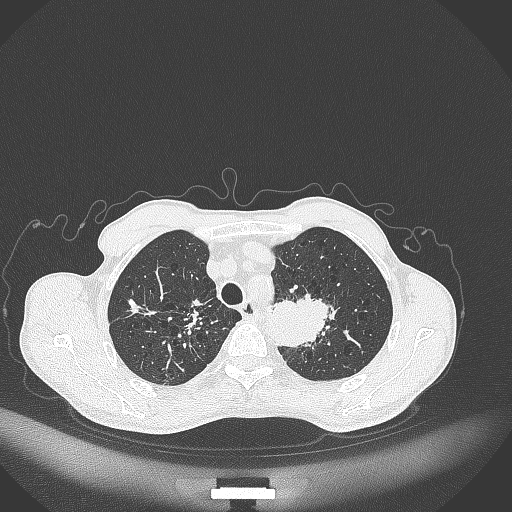
Chest CT, one axial slice. Slice 345 of 386 in the series (ordered by position). Reconstruction kernel B70f. 120 kVp. Lung window (W 1500 / L -600 HU). 1 mm slice thickness. 512 × 512 image matrix, field of view 400 × 400 mm. Patient: male, 65 years. Case-level facts recorded for this patient, not image findings: clinical TNM (as recorded): T2b N0 M0.
Annotated regions visible in this slice (bounding box drawn by a radiologist):
- lung tumour (recorded histology: adenocarcinoma): bounding box (x1, y1, x2, y2) in pixels: (265, 289, 330, 348)